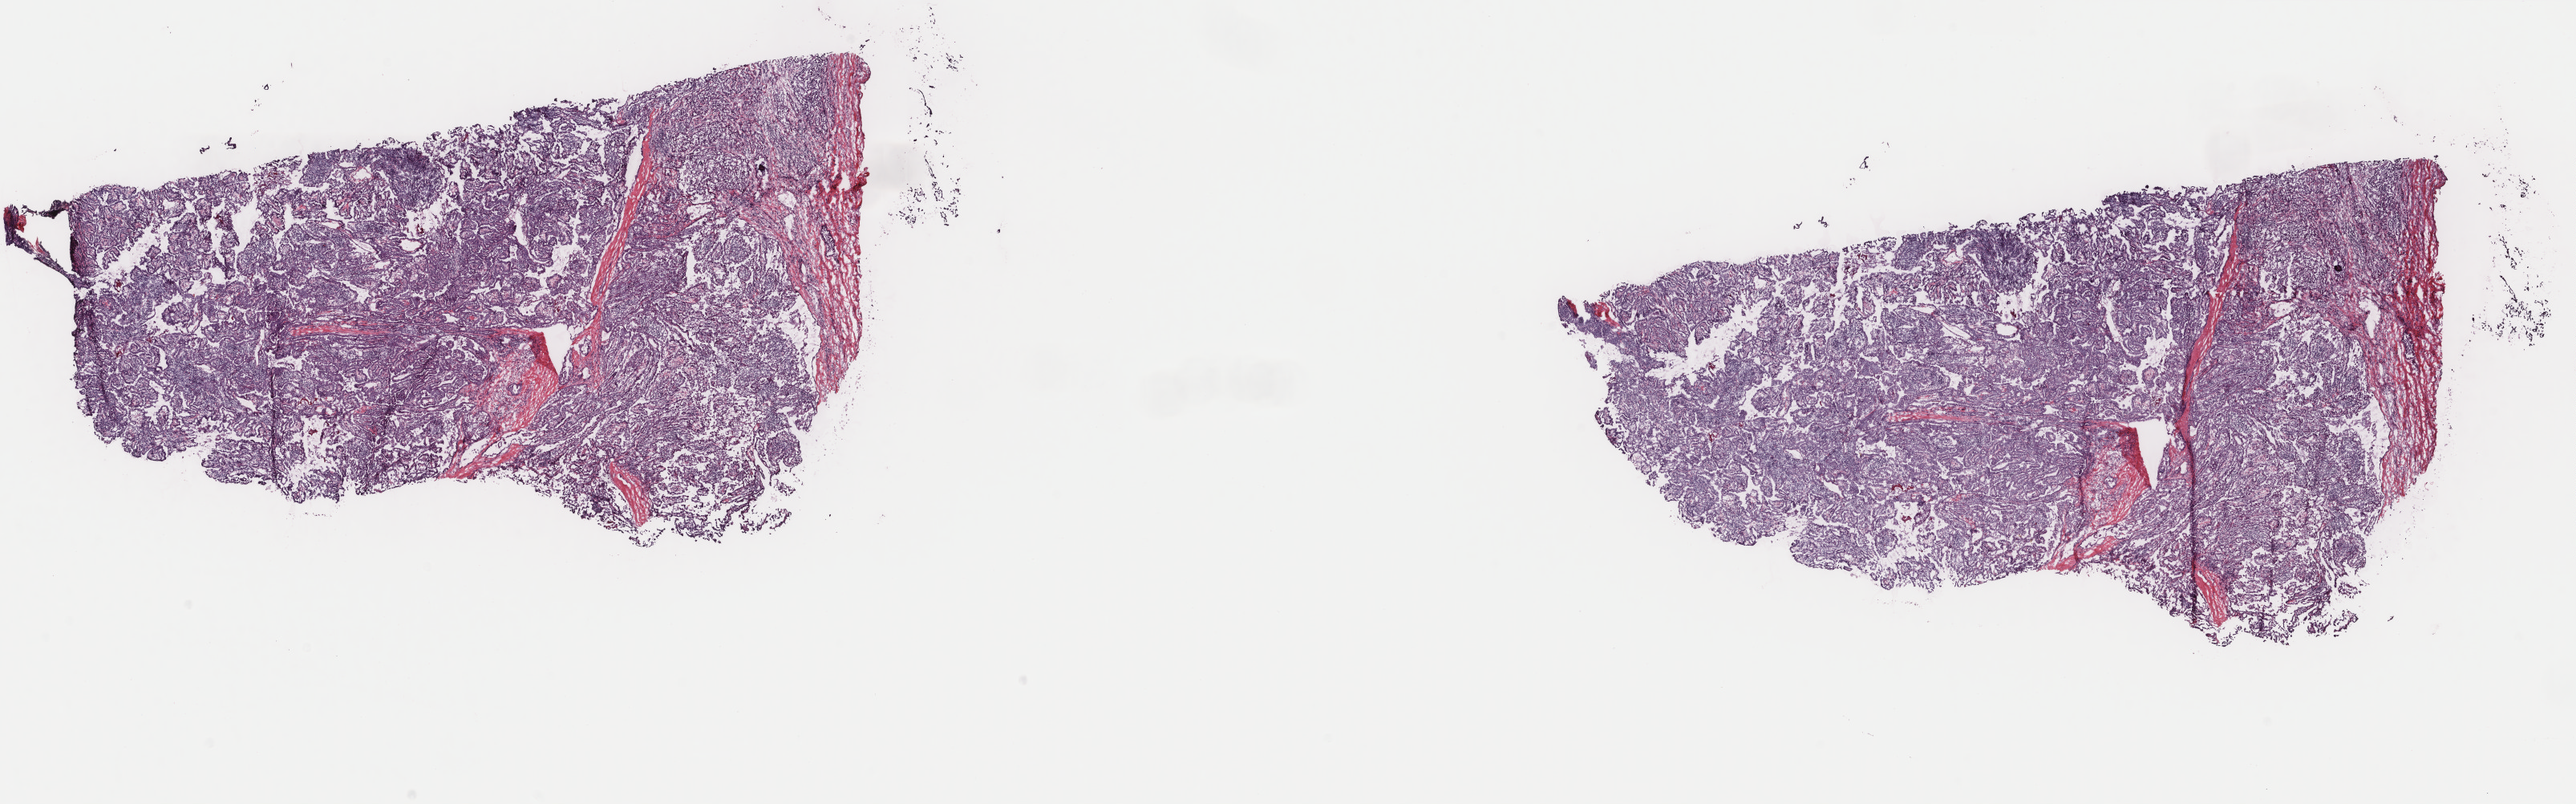
Whole-slide histology image, H&E-stained — shown as a low-resolution overview of the whole scanned area (about 25.5 x 8.0 mm), frozen section from the top of the tissue portion, thyroid, primary tumour sample. Female patient; age at initial diagnosis 30 years. Slide review estimates, as recorded: tumour cells 85%, tumour nuclei 85%, normal cells 0%, stromal cells 15%, necrosis 0%. Inflammatory infiltration, as recorded: lymphocyte infiltration 3%, monocyte infiltration 1%, neutrophil infiltration 1%.
• AJCC pathologic stage: I
• laterality: left
• lymph nodes positive (case pathology): 1 of 5 examined
• diagnosis: Papillary adenocarcinoma, NOS